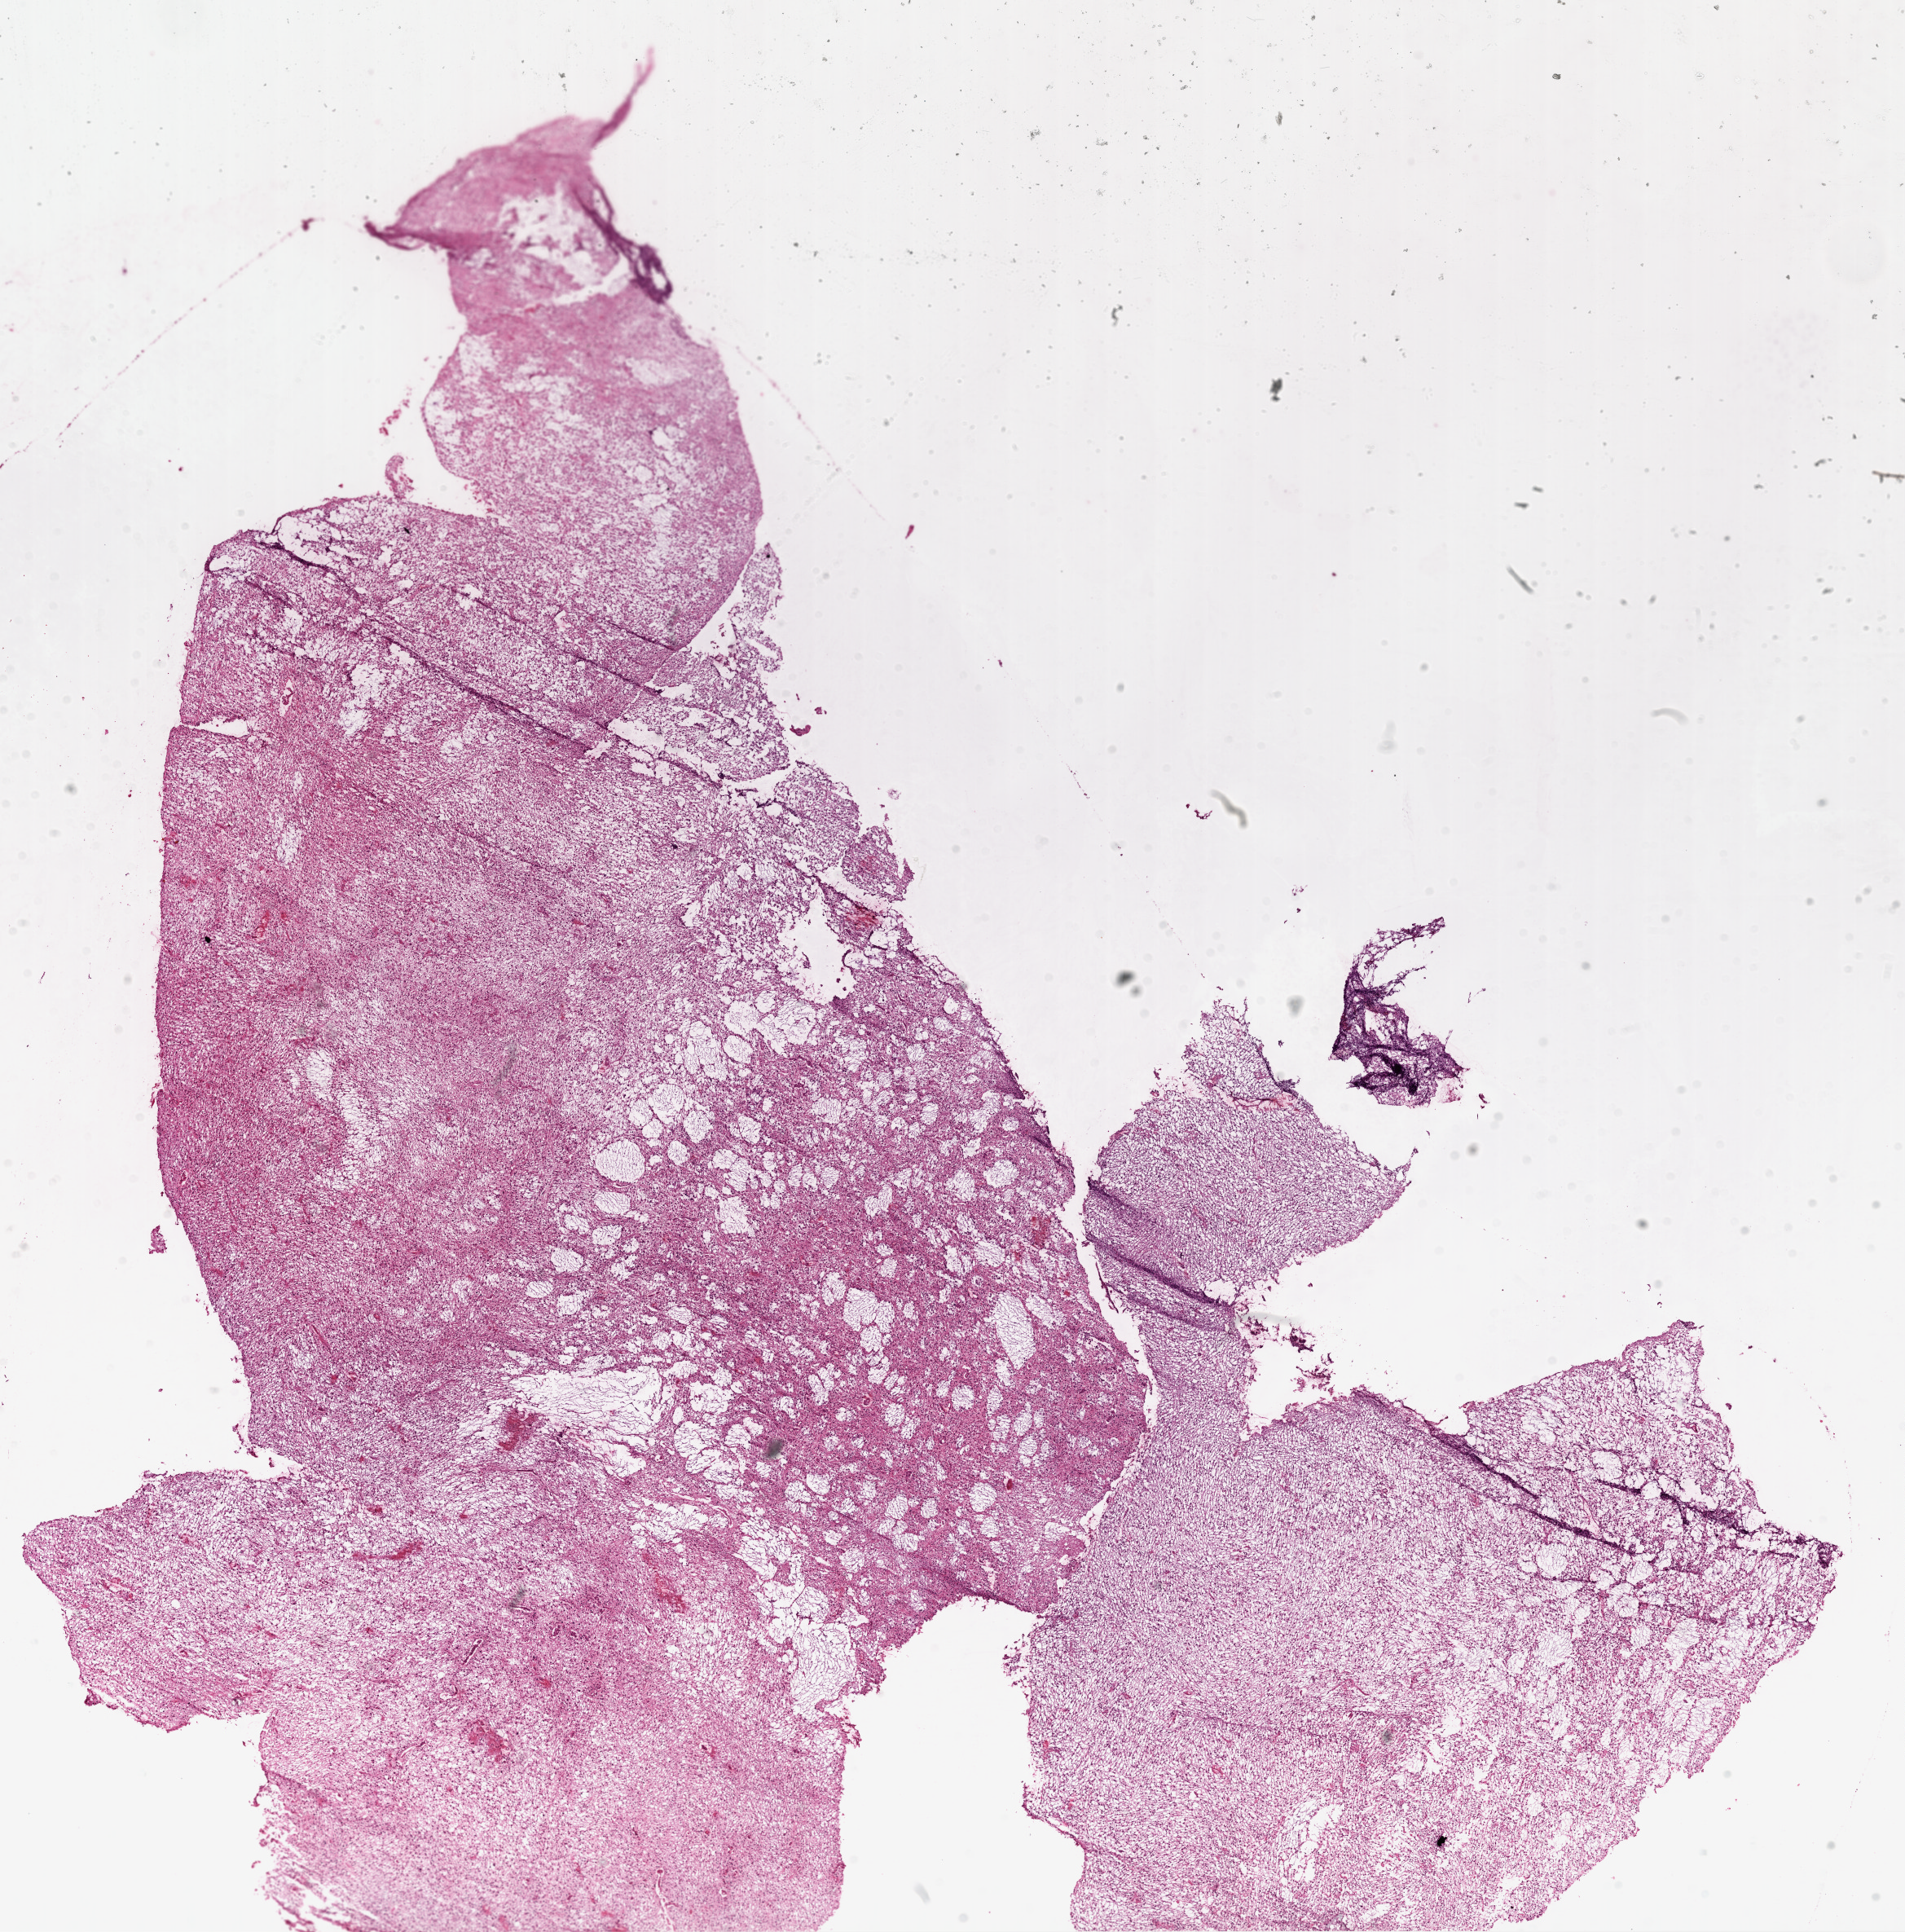
Whole-slide histology image, H&E-stained, shown as a low-resolution overview of the whole scanned area (about 18.9 x 19.1 mm, from a 20x scan). Frozen section from the top of the tissue portion. Primary tumour sample from the brain. Male patient; age at initial diagnosis 28 years. Pathologist review of this section (percent, as recorded): tumour cells 80%, tumour nuclei 100%, normal cells 0%, stromal cells 0%, necrosis 20%.
* diagnosis: Glioblastoma